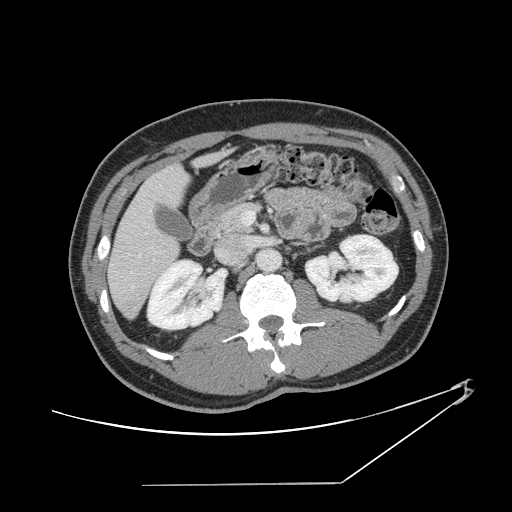
Contrast-enhanced abdominal CT, one axial slice; slice 66 of 152 in the series (ordered by position); 120 kVp; intravenous contrast given; soft-tissue window (W 400 / L 40 HU); 2.5 mm slice thickness; 512 × 512 image matrix. Male patient, age 45 years. Case-level facts recorded for this patient, not image findings: diagnosis: colorectal cancer liver metastases, imaged before liver resection; multiple liver metastases: no; largest metastasis: 1 cm; disease in both lobes: no.
Structures marked on this image (manually delineated by an expert):
- hepatic veins: bounding box [x1, y1, x2, y2] px = [138, 210, 156, 258]
- liver: [109, 153, 224, 317]
- planned liver remnant (the part of the liver to remain after resection): [109, 167, 187, 317]
- portal vein (with intrahepatic branches): [242, 211, 255, 225]